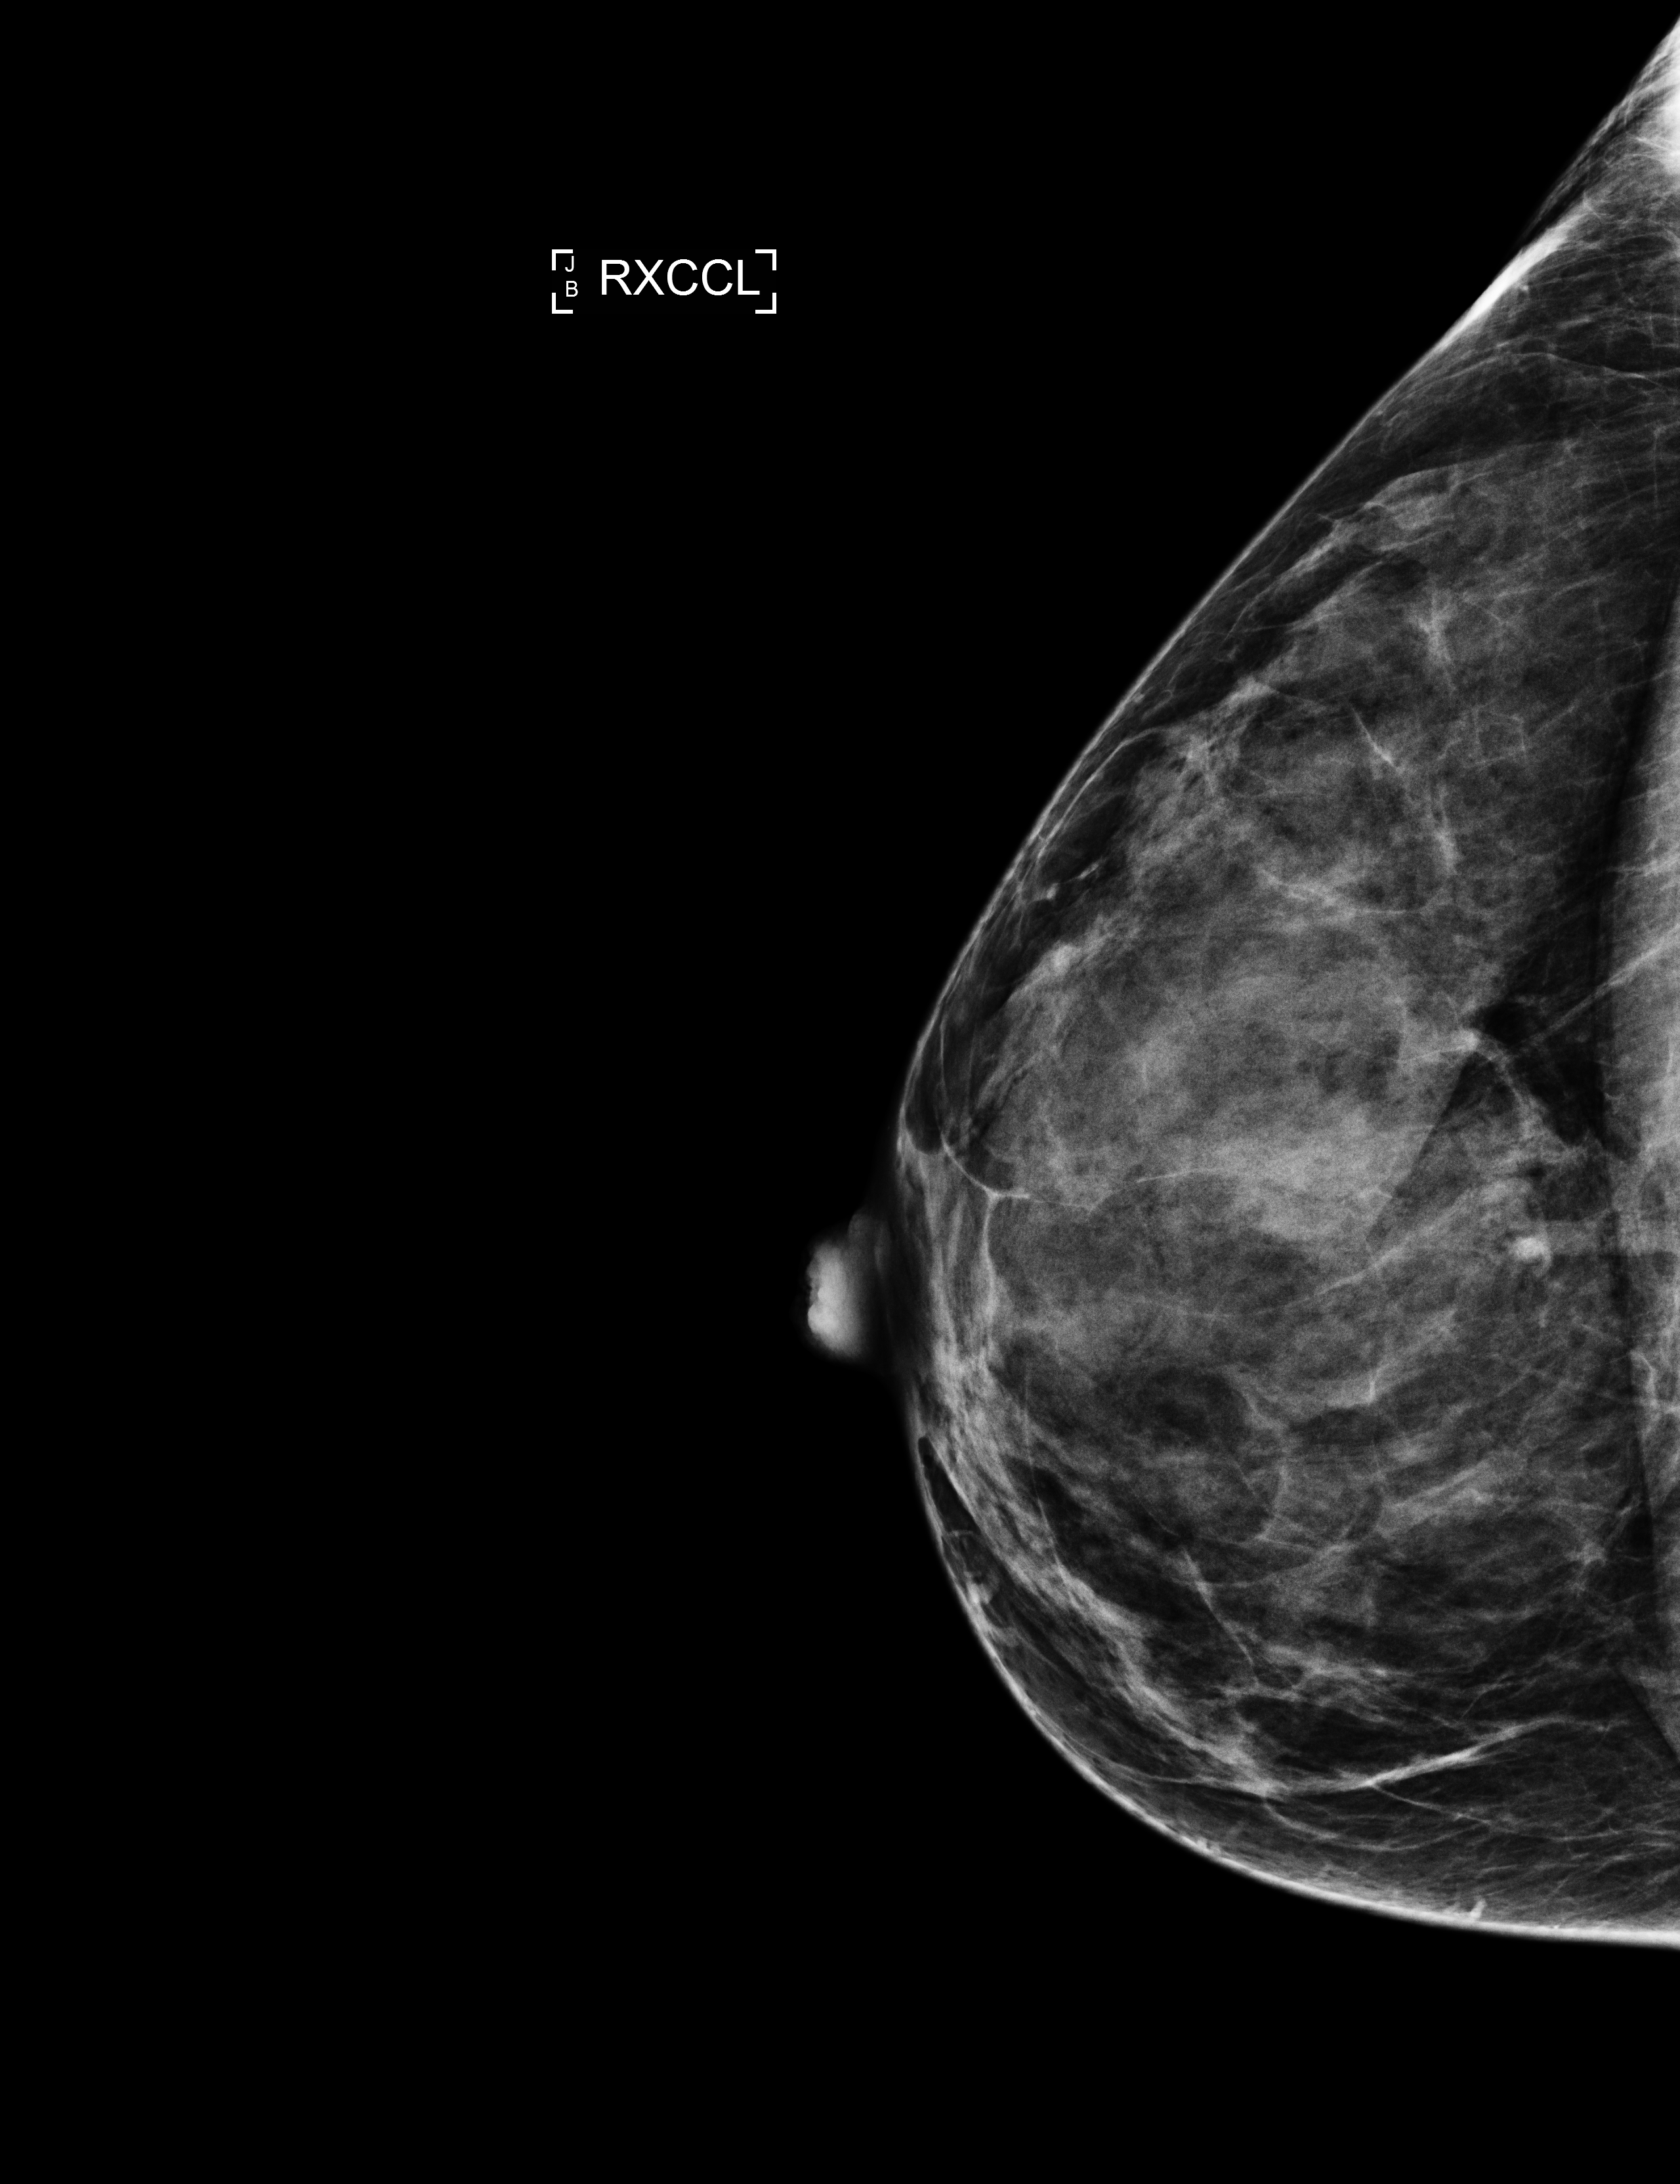
Screening examination; compressed breast thickness 40 mm. Female patient, age 47 years.
Image type: full-field digital mammogram. Breast: right. Projection: exaggerated CC view (lateral).